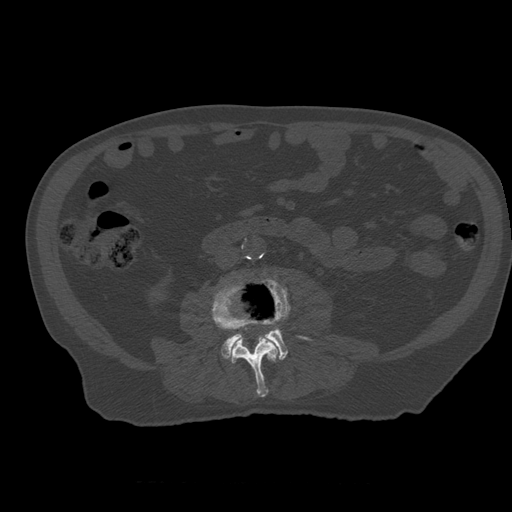
CT including the spine, one axial slice. Slice 179 of 399 in the series (ordered by position). 120 kVp. Bone window (W 1800 / L 400 HU). 1.25 mm slice thickness. 512 × 512 image matrix. Patient age 73 years. From the clinical record (not read from this slice): primary cancer: prostate; vertebrae with lytic lesions (as recorded): L2.
Outlined on this slice (semi-automatically segmented with operator editing):
- L3 vertebra: box from (x=211, y=282) to (x=280, y=398) px
- L4 vertebra: (x=221, y=280)–(x=308, y=361)